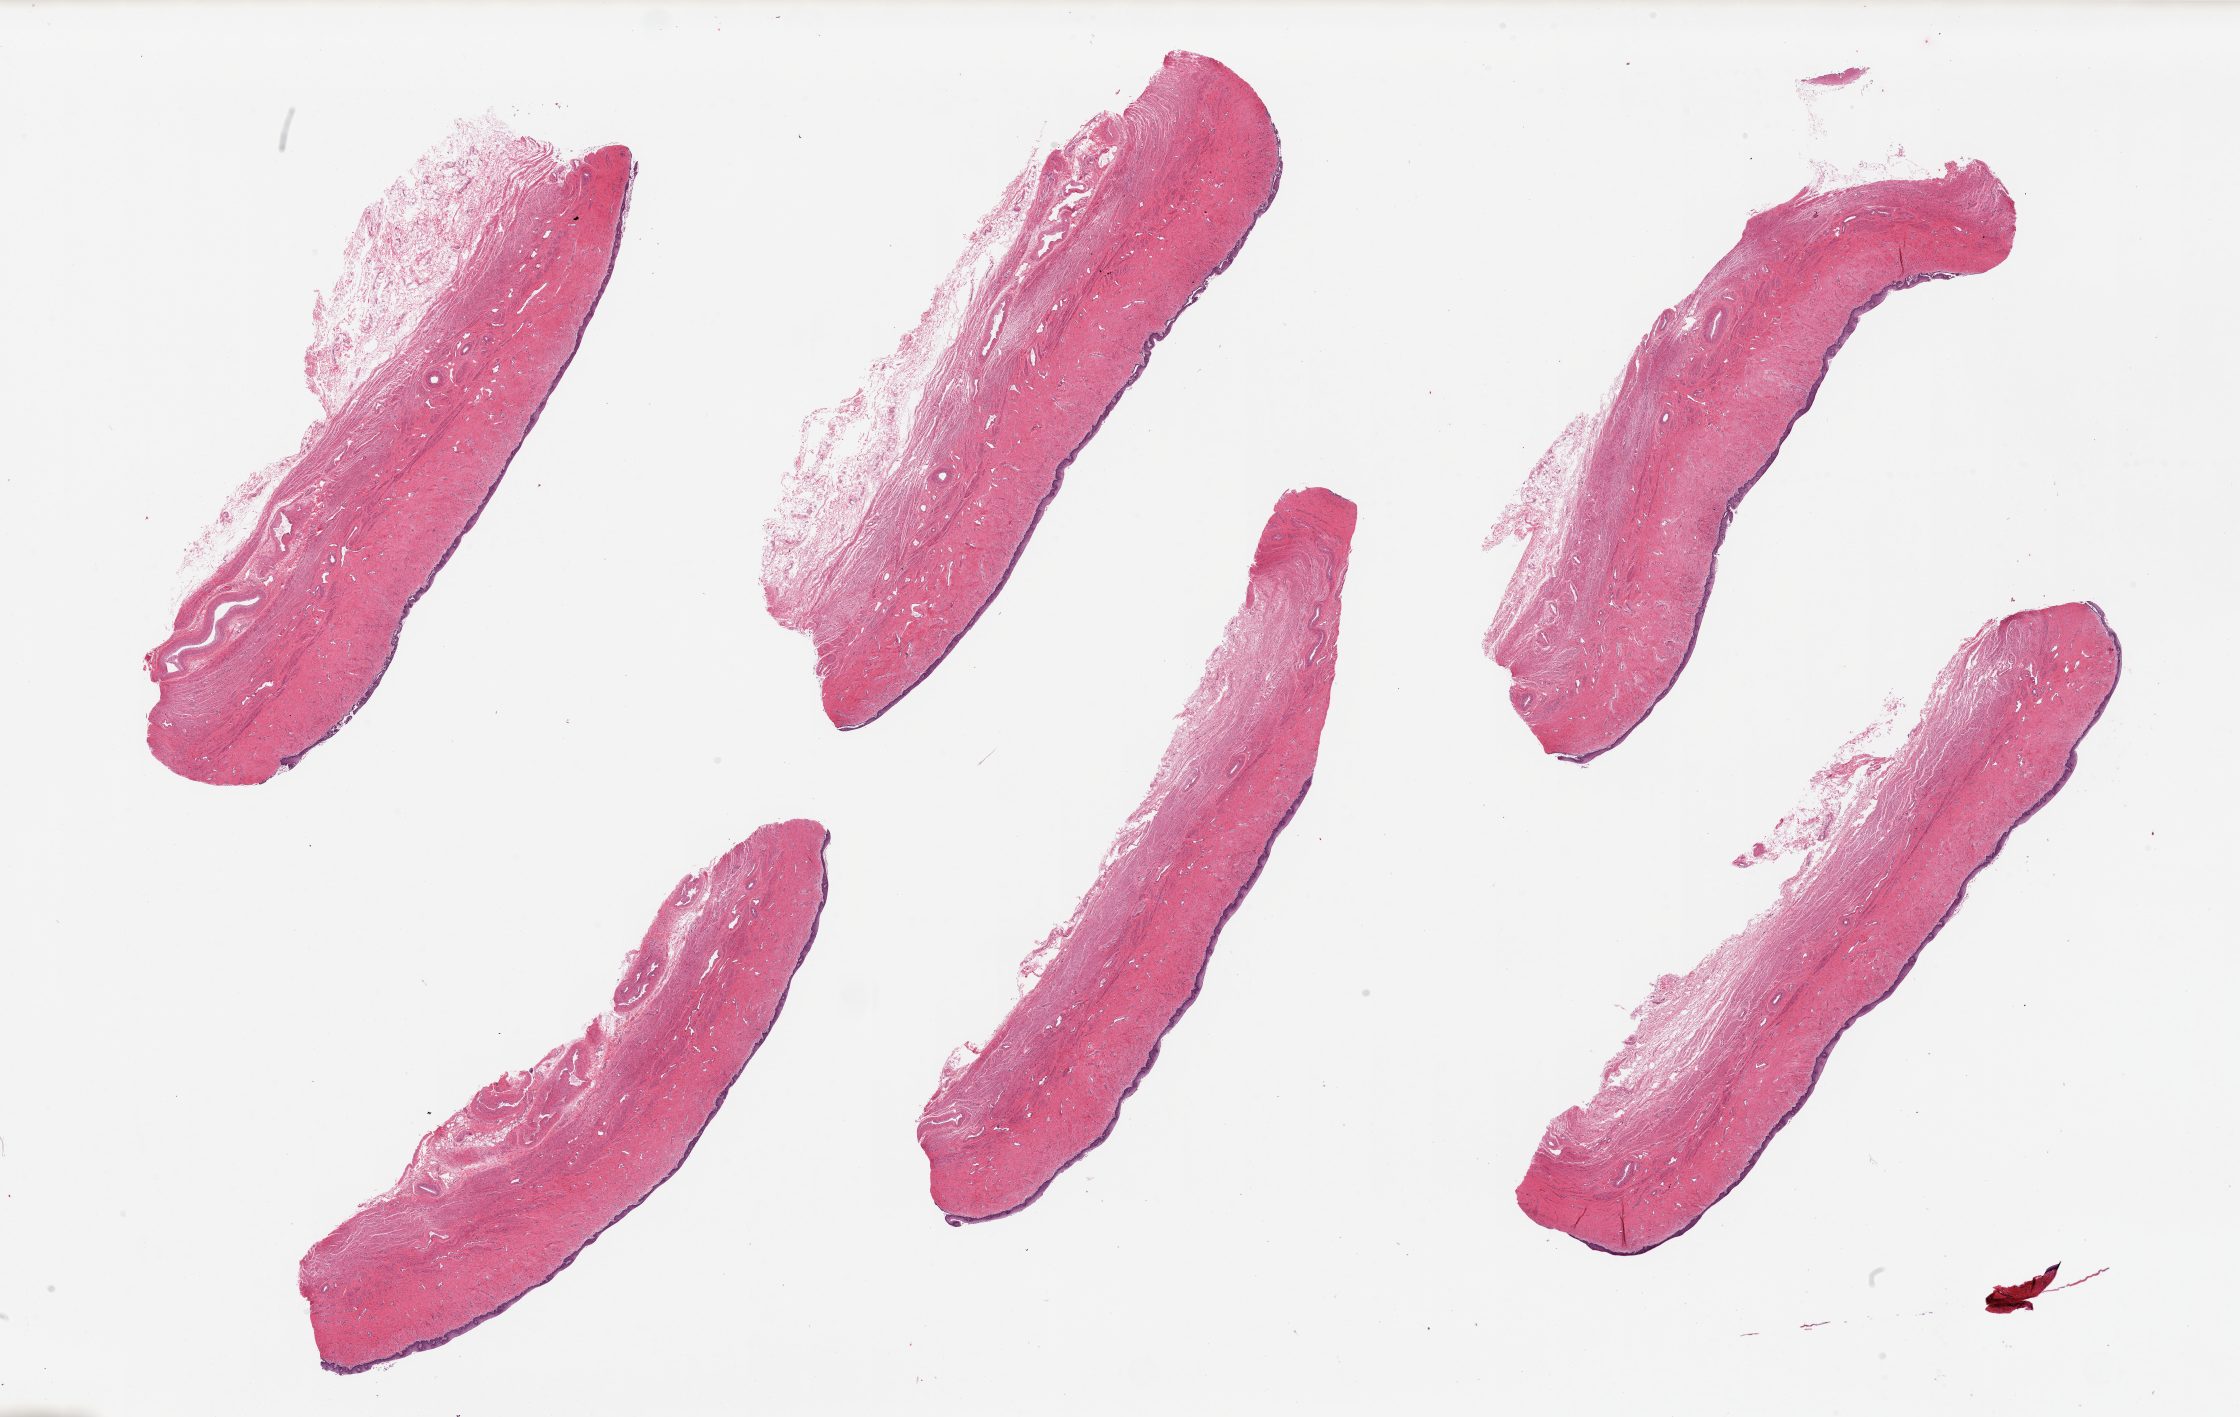
Whole-slide image, H&E stain, a low-resolution overview of the entire scanned area, about 35.4 x 22.4 mm (from a 20x scan). PAXgene-fixed paraffin-embedded (PFPE) section. Target tissue: vagina. Donor tissue sample. Donor: female.
Pathologist's review note for this sample: 6 pieces.